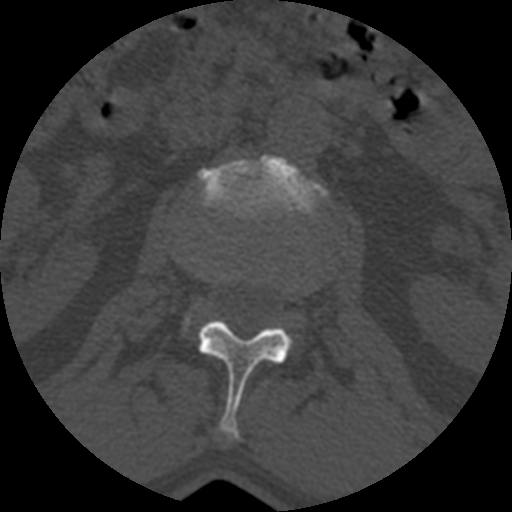
CT including the spine, one axial slice. Slice 351 of 399 in the series (ordered by position). Reconstruction kernel STANDARD. Bone window (W 1800 / L 400 HU). 1.25 mm slice thickness. 512 × 512 image matrix, field of view 160 × 160 mm. Patient age 71 years. From the clinical record (not read from this slice): primary cancer: prostate.
Structures marked on this image (semi-automatic segmentation, software-assisted and operator-edited):
- L1 vertebra: bounding box (x1, y1, x2, y2) in pixels: (197, 319, 292, 441)
- L2 vertebra: (197, 155, 327, 218)